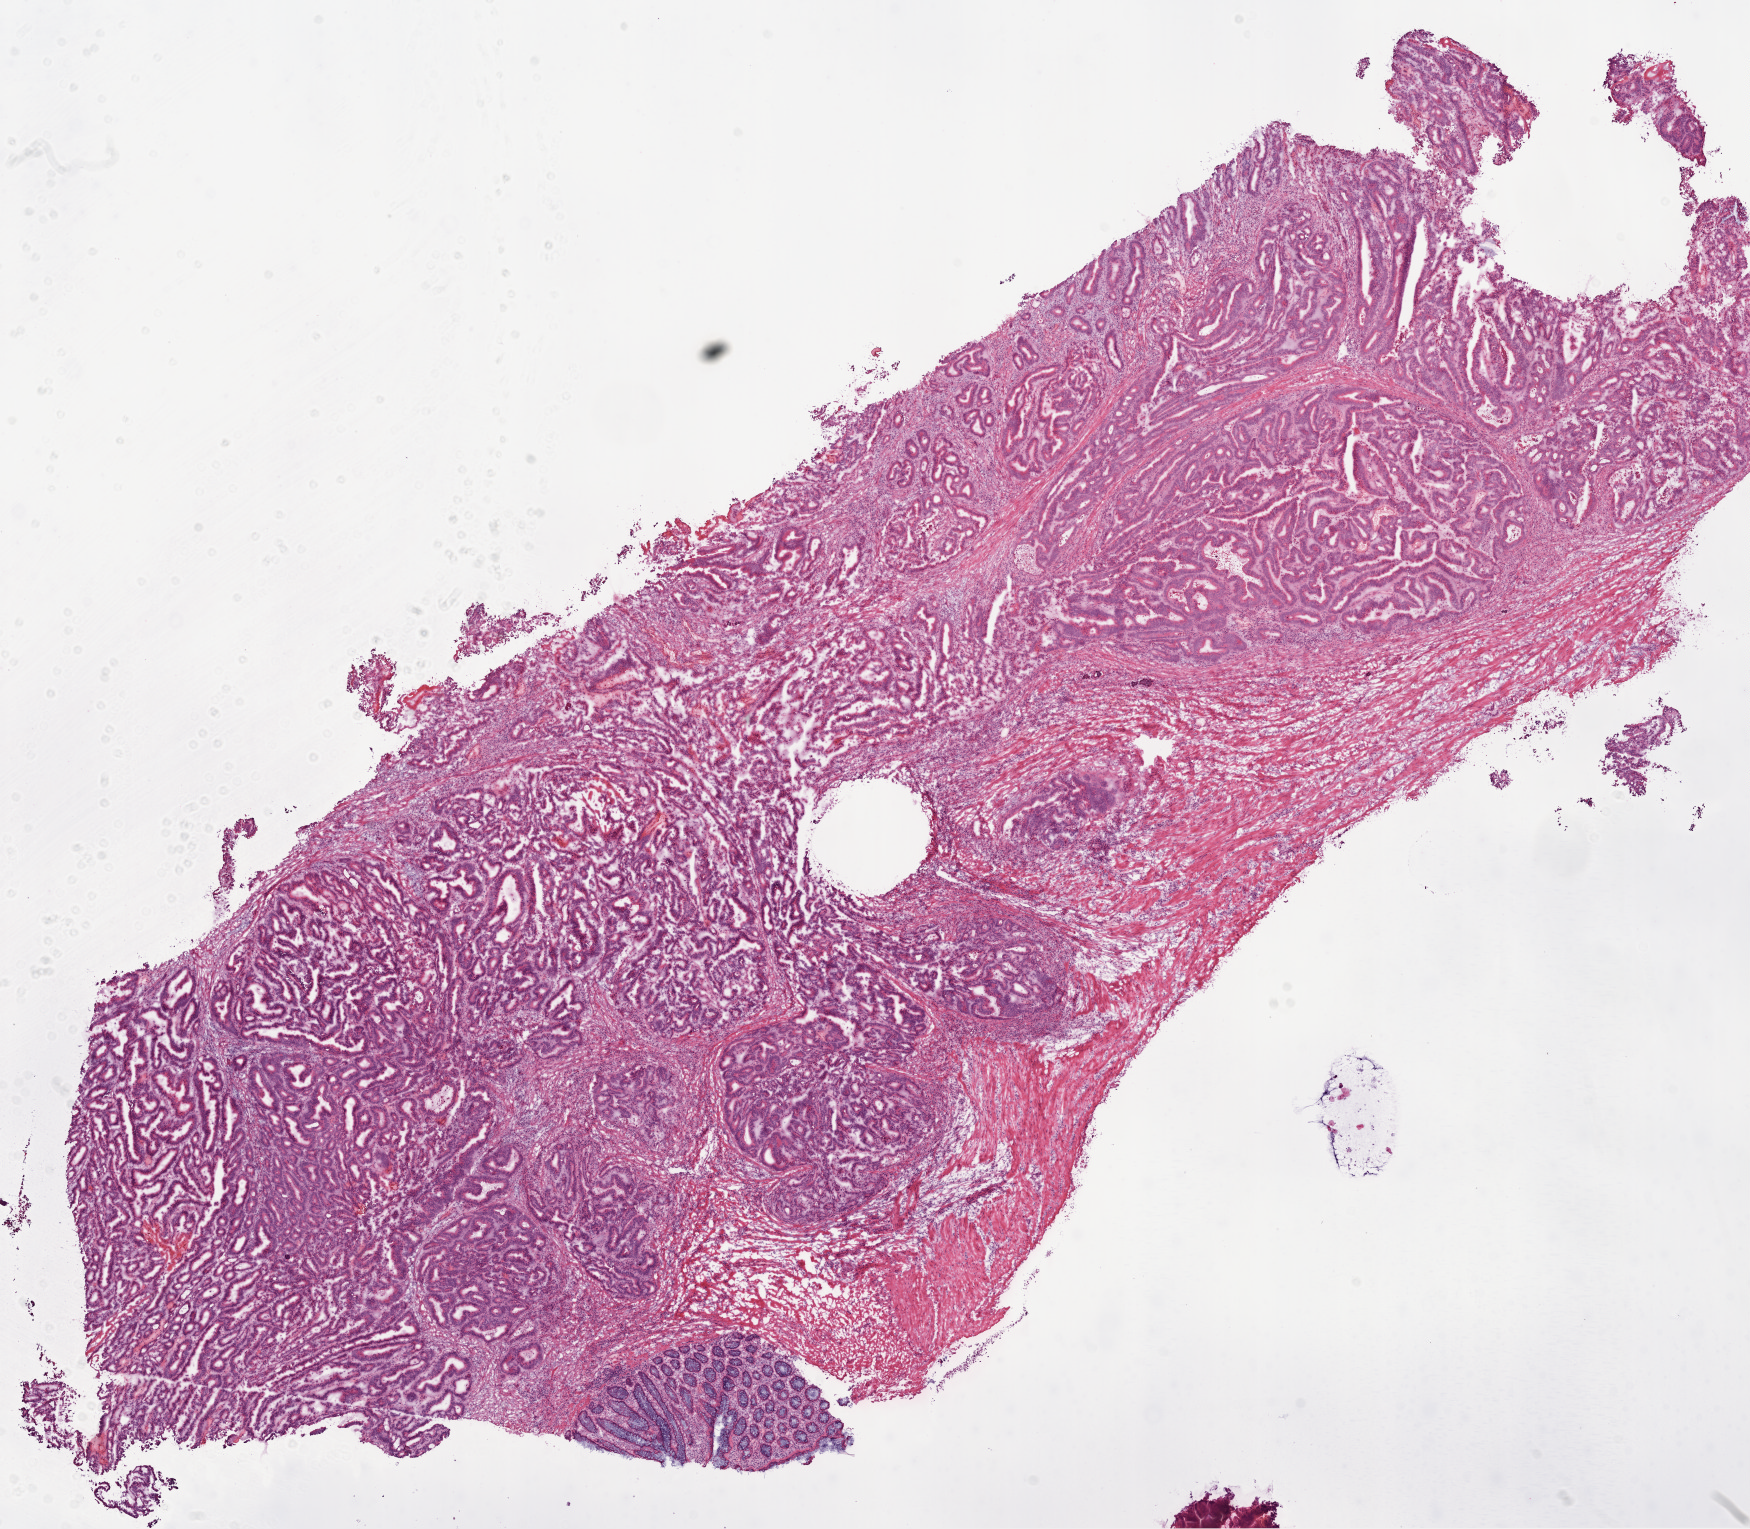
Digitized H&E-stained tissue section (whole slide) — a low-resolution overview of the entire scanned area, about 14.0 x 12.3 mm (acquisition: 20x scan); frozen section; sample: primary tumour, colon. Male, age 56 years at initial diagnosis. Composition of this section per pathologist review: tumour cells 80%, tumour nuclei 80%, normal cells 5%, stromal cells 15%, necrosis 0%.
• diagnosis: Adenocarcinoma, NOS
• AJCC pathologic stage: IIA